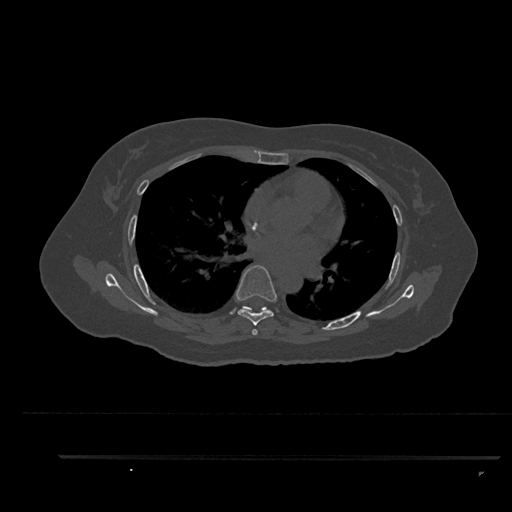
CT including the spine, one axial slice. Slice 550 of 797 in the series (ordered by position). 120 kVp. Bone window (W 1800 / L 400 HU). 512 × 512 image matrix, field of view 408 × 408 mm. Patient: female, 44 years. From the clinical record (not read from this slice): primary cancer: renal.
Outlined on this slice (semi-automatically segmented with operator editing):
- T6 vertebra: bounding box <236,265,277,335> (left, top, right, bottom; pixels)
- T7 vertebra: <242,306,267,313>